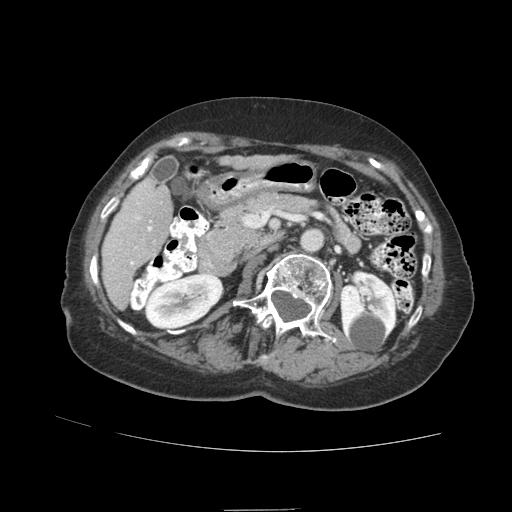
Contrast-enhanced abdominal CT (liver protocol), one axial slice; 140 kVp; soft-tissue window (W 400 / L 40 HU); 2.5 mm slice thickness; 512 × 512 image matrix, field of view 360 × 360 mm. From the clinical record (not read from this slice): diagnosis: hepatocellular carcinoma (patient treated with transarterial chemoembolisation; whether this scan precedes or follows treatment is not stated here); TNM stage (as recorded): Stage-II; Child-Pugh class: A; tumour differentiation: moderately differentiated; tumour size: 4 cm.
Structures marked on this image (semi-automatically segmented with operator editing):
- liver parenchyma outside the tumour (the mass and vessels are separate outlines, so this box may not span the whole liver): bounding box [x1, y1, x2, y2] px = [102, 176, 172, 309]
- liver vessels: [131, 186, 152, 265]